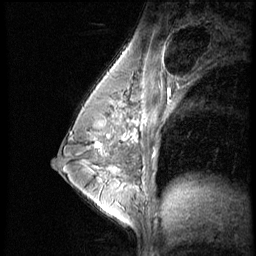
Breast MRI (dynamic contrast-enhanced), one sagittal slice; slice 35 of 56 in the series (ordered by position); dynamic contrast-enhanced series, image 2 of 4 at this slice position (ordered by acquisition); 1.5 T; TE 4.2 ms, TR 8.9 ms; 256 × 256 image matrix. Female patient, age 35 years. From the clinical record (not read from this slice): setting: breast cancer imaged before/during neoadjuvant chemotherapy; receptor status: HER2-positive.
Outlined on this slice (semi-automatic segmentation, software-assisted and operator-edited):
- analysis volume of interest (the breast-tissue region the enhancement analysis was run in; not a lesion): bounding box [x1, y1, x2, y2] px = [73, 111, 131, 164]
- tumour enhancement mask (voxels above the 140 % enhancement threshold inside the analysis volume of interest): [97, 142, 103, 146]